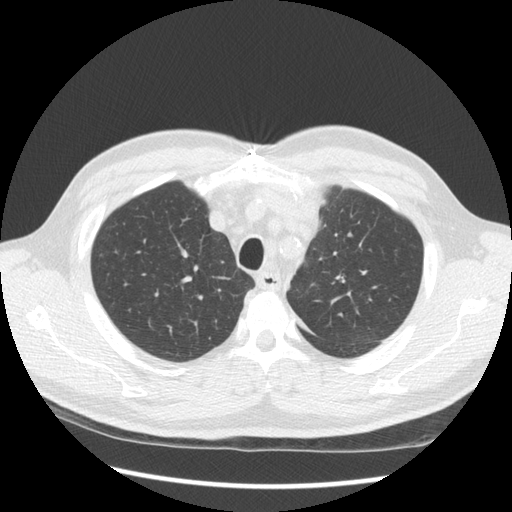
Low-dose screening chest CT, one axial slice. Slice 111 of 136 in the series (ordered by position). Lung window (W 1500 / L -600 HU). 2.5 mm slice thickness. 512 × 512 image matrix, field of view 360 × 360 mm.
Structures marked on this image (outlined manually by an expert reader):
- lesion 1 (tumor, upper lobe of left lung): bounding box <304,191,322,229> (left, top, right, bottom; pixels)